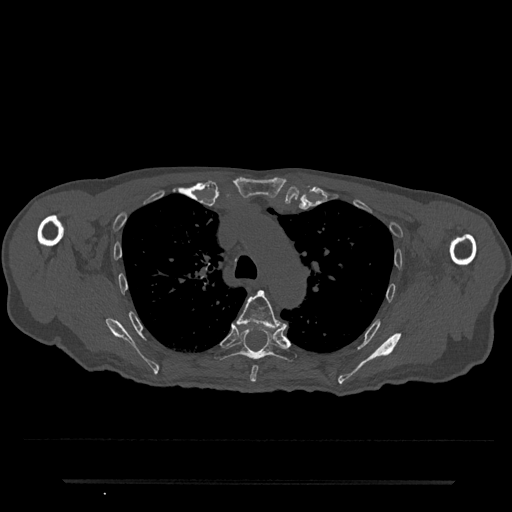
CT including the spine, one axial slice; position 552 of 797 along the scan axis; bone window (W 1800 / L 400 HU); 0.5 mm slice thickness; 512 × 512 image matrix, field of view 427 × 427 mm. Male patient, age 74 years. From the clinical record (not read from this slice): primary cancer: prostate.
Annotated regions visible in this slice (semi-automatically segmented with operator editing):
- T5 vertebra: bounding box <236,290,288,382> (left, top, right, bottom; pixels)
- T6 vertebra: <215,328,297,362>